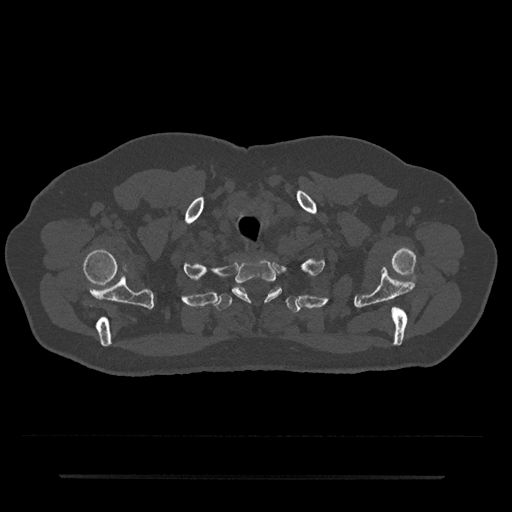
CT including the spine, one axial slice. Slice 630 of 797 in the series (ordered by position). Reconstruction kernel Br40s/3. Bone window (W 1800 / L 400 HU). 0.5 mm slice thickness. 512 × 512 image matrix, field of view 437 × 437 mm. Patient: male, 69 years. From the clinical record (not read from this slice): primary cancer: prostate.
Outlined on this slice (semi-automatically segmented with operator editing):
- T1 vertebra: bounding box <232,260,282,302> (left, top, right, bottom; pixels)
- T2 vertebra: <216,287,300,313>